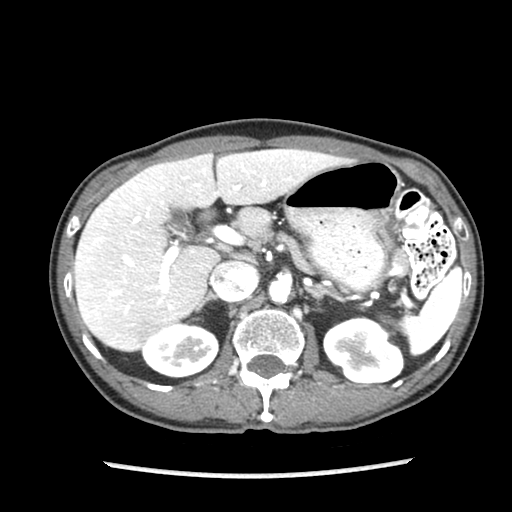
Contrast-enhanced abdominal CT (liver protocol), one axial slice. 140 kVp. Soft-tissue window (W 400 / L 40 HU). 2.5 mm slice thickness. 512 × 512 image matrix, field of view 300 × 300 mm. From the clinical record (not read from this slice): diagnosis: hepatocellular carcinoma (patient treated with transarterial chemoembolisation; whether this scan precedes or follows treatment is not stated here); TNM stage (as recorded): Stage-IIIB; Child-Pugh class: A.
Structures marked on this image (semi-automatically segmented with operator editing):
- liver parenchyma outside the tumour (the mass and vessels are separate outlines, so this box may not span the whole liver): bounding box [x1, y1, x2, y2] px = [74, 148, 349, 350]
- liver vessels: [84, 152, 288, 315]